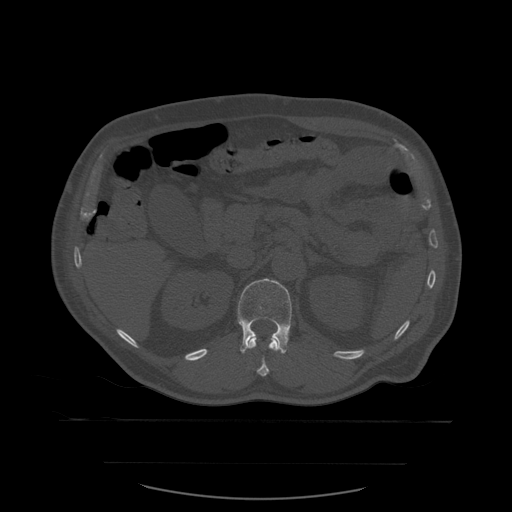
CT including the spine, one axial slice. Slice 255 of 590 in the series (ordered by position). Bone window (W 1800 / L 400 HU). 1.25 mm slice thickness. 512 × 512 image matrix, field of view 479 × 479 mm. Patient age 71 years. From the clinical record (not read from this slice): primary cancer: lung; vertebrae with lytic lesions (as recorded): T1, T2, L5, S1.
Annotated regions visible in this slice (semi-automatic segmentation, software-assisted and operator-edited):
- L1 vertebra: bounding box [x1, y1, x2, y2] px = [238, 279, 292, 352]
- T12 vertebra: [240, 336, 286, 377]